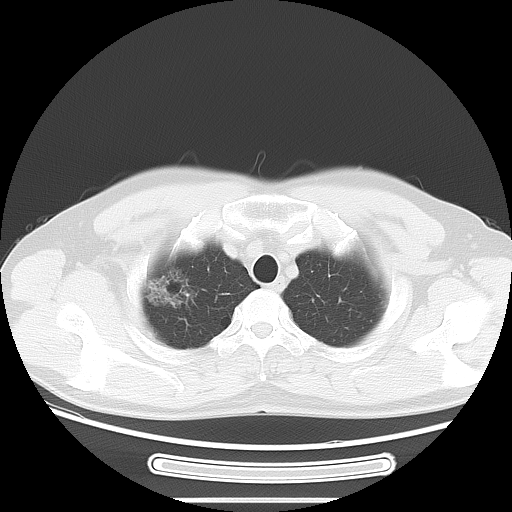
Chest CT, one axial slice. Position 58 of 68 along the scan axis. Lung window (W 1500 / L -600 HU). 512 × 512 image matrix. Male patient, age 53 years. From the clinical record (not read from this slice): clinical TNM (as recorded): T1c N0 M0; histopathological grade: G2.
Structures marked on this image (rectangle marked by the reading radiologist):
- lung tumour (recorded histology: adenocarcinoma): bounding box (x1, y1, x2, y2) in pixels: (135, 259, 204, 318)